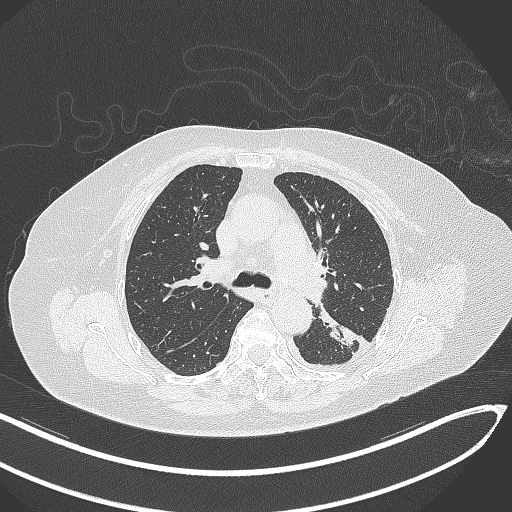
Chest CT, one axial slice; slice 205 of 270 in the series (ordered by position); reconstruction kernel B70f; 120 kVp; lung window (W 1500 / L -600 HU); 1 mm slice thickness; 512 × 512 image matrix, field of view 400 × 400 mm. Patient: female, 76 years. Case-level facts recorded for this patient, not image findings: clinical TNM (as recorded): T1c N0 M0.
Outlined on this slice (bounding box drawn by a radiologist):
- lung tumour (recorded histology: adenocarcinoma): box from (x=312, y=300) to (x=367, y=353) px